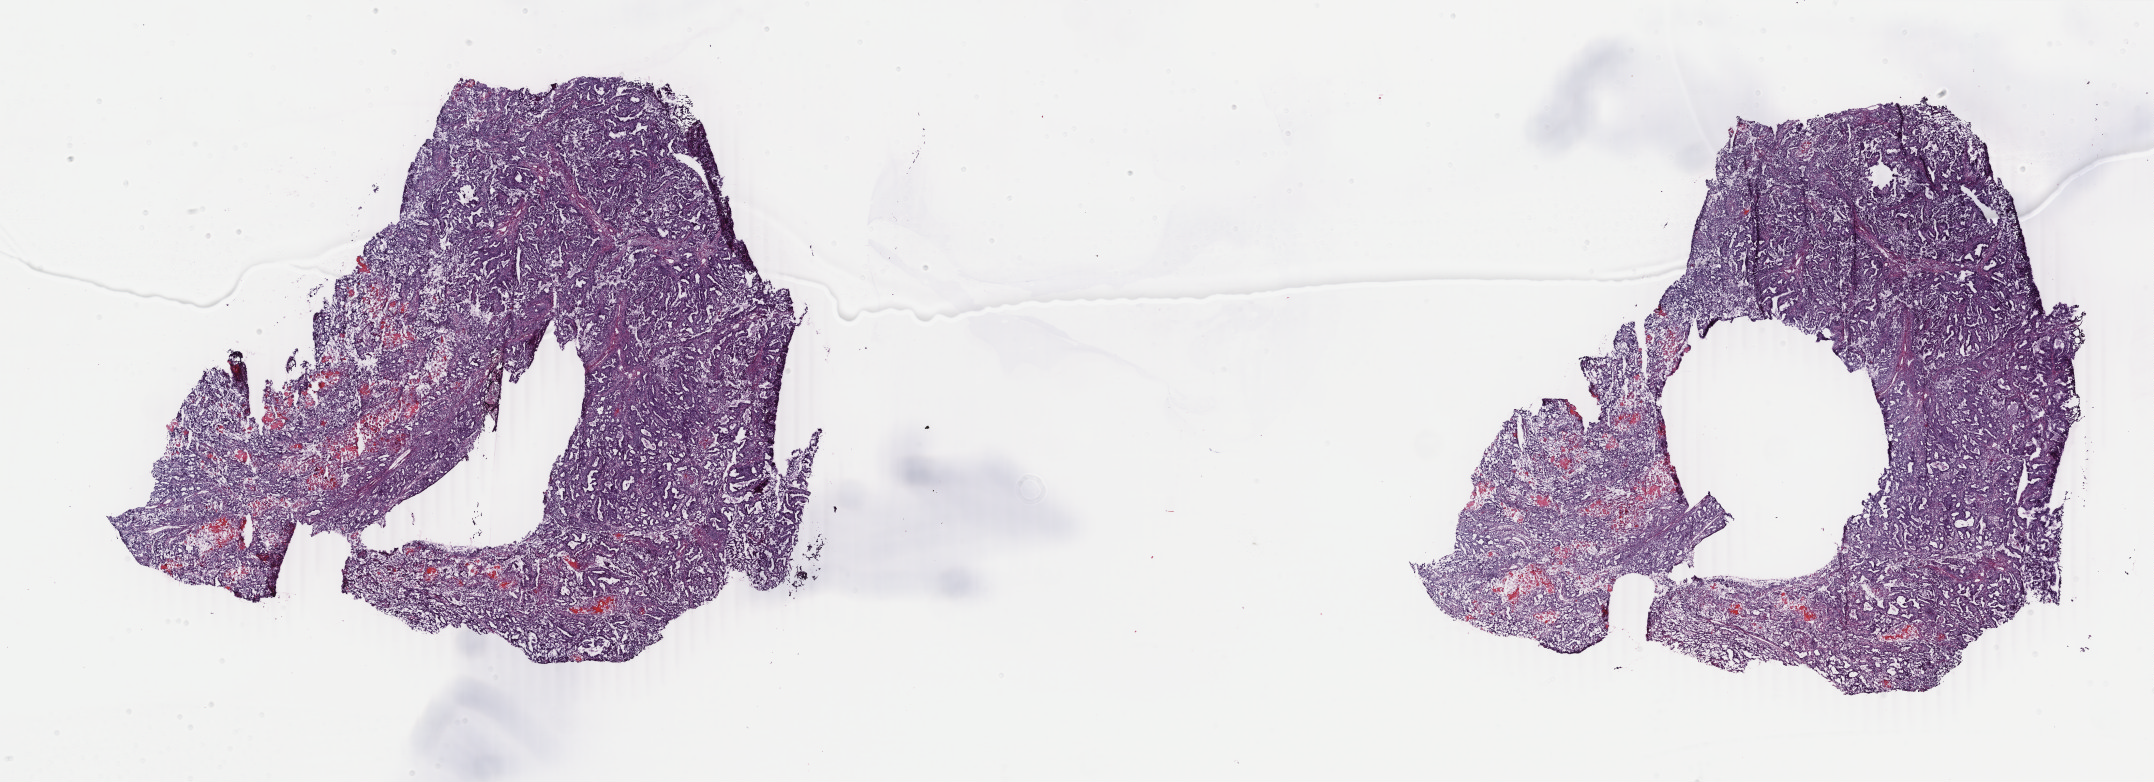
Whole-slide histology image, H&E, a low-resolution overview of the entire scanned area, about 34.3 x 12.4 mm. Frozen section from the bottom of the tissue portion. Uterus, primary tumour sample. Female, age 83 years at initial diagnosis. Histologic grade: G2 (moderately differentiated). Pathologist review of this section (percent, as recorded): tumour cells 80%, tumour nuclei 88%, normal cells 0%, stromal cells 8%, necrosis 12%. Inflammatory infiltration, as recorded: lymphocyte infiltration 5%, monocyte infiltration 2%, neutrophil infiltration 1%.
Histologic diagnosis: Endometrioid adenocarcinoma, NOS (endometrium). FIGO stage: IA. Lymph nodes positive (case pathology): 0 of 13 examined.